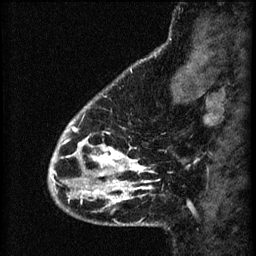
Breast MRI (dynamic contrast-enhanced), one sagittal slice; slice 13 of 60 in the series (ordered by position); 3 images stored at this slice position (order not interpretable as contrast timing); 1.5 T; TE 4.2 ms, TR 8.2 ms; 2.2 mm slice thickness; 256 × 256 image matrix, field of view 180 × 180 mm. Female patient, age 41 years.
Structures marked on this image (semi-automatic segmentation, software-assisted and operator-edited):
- analysis volume of interest (the breast-tissue region the enhancement analysis was run in; not a lesion): box from (x=56, y=104) to (x=157, y=207) px
- tumour enhancement mask (voxels above the 70 % enhancement threshold inside the analysis volume of interest): (x=56, y=106)–(x=154, y=205)